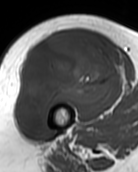
MRI of an extremity soft-tissue mass, one axial slice; slice 61 of 99 in the series (ordered by position); MR volume resampled by the dataset authors to the PET/CT grid (not the native acquisition matrix); 3.27 mm slice thickness; 138 × 172 image matrix, field of view 135 × 168 mm. Female patient. From the clinical record (not read from this slice): histological type: pleiomorphic undifferentiated sarcoma; grade: high; site of the primary tumour: right quadricep.
Annotated regions visible in this slice (expert contour drawn on MRI and transferred to this co-registered scan by the dataset authors):
- gross tumour volume including surrounding oedema: box from (x=16, y=34) to (x=118, y=131) px
- gross tumour volume (mass): (x=16, y=34)–(x=118, y=131)